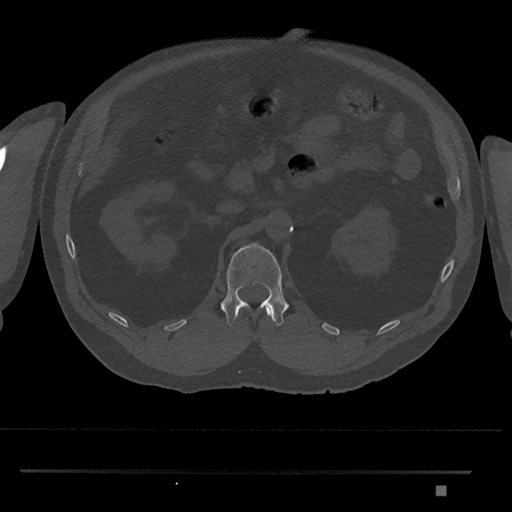
CT including the spine, one axial slice; position 835 of 1134 along the scan axis; bone window (W 1800 / L 400 HU); 0.5 mm slice thickness; 512 × 512 image matrix, field of view 429 × 429 mm. Male patient, age 65 years. From the clinical record (not read from this slice): primary cancer: prostate.
Outlined on this slice (semi-automatic segmentation, software-assisted and operator-edited):
- L1 vertebra: box from (x=220, y=243) to (x=289, y=326) px
- T12 vertebra: (x=266, y=308)–(x=272, y=317)